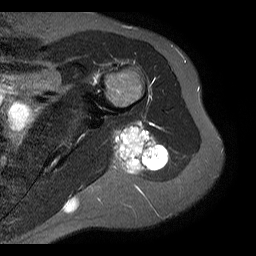
MRI of an extremity soft-tissue mass, one axial slice; position 10 of 20 along the scan axis; STIR; 4 mm slice thickness; 256 × 256 image matrix, field of view 150 × 150 mm. Female patient. Case-level facts recorded for this patient, not image findings: histological type: malignant fibrous histiocytoma; grade: low; site of the primary tumour: left arm.
Annotated regions visible in this slice (manually delineated by an expert):
- gross tumour volume (mass): bounding box [x1, y1, x2, y2] px = [112, 122, 168, 174]